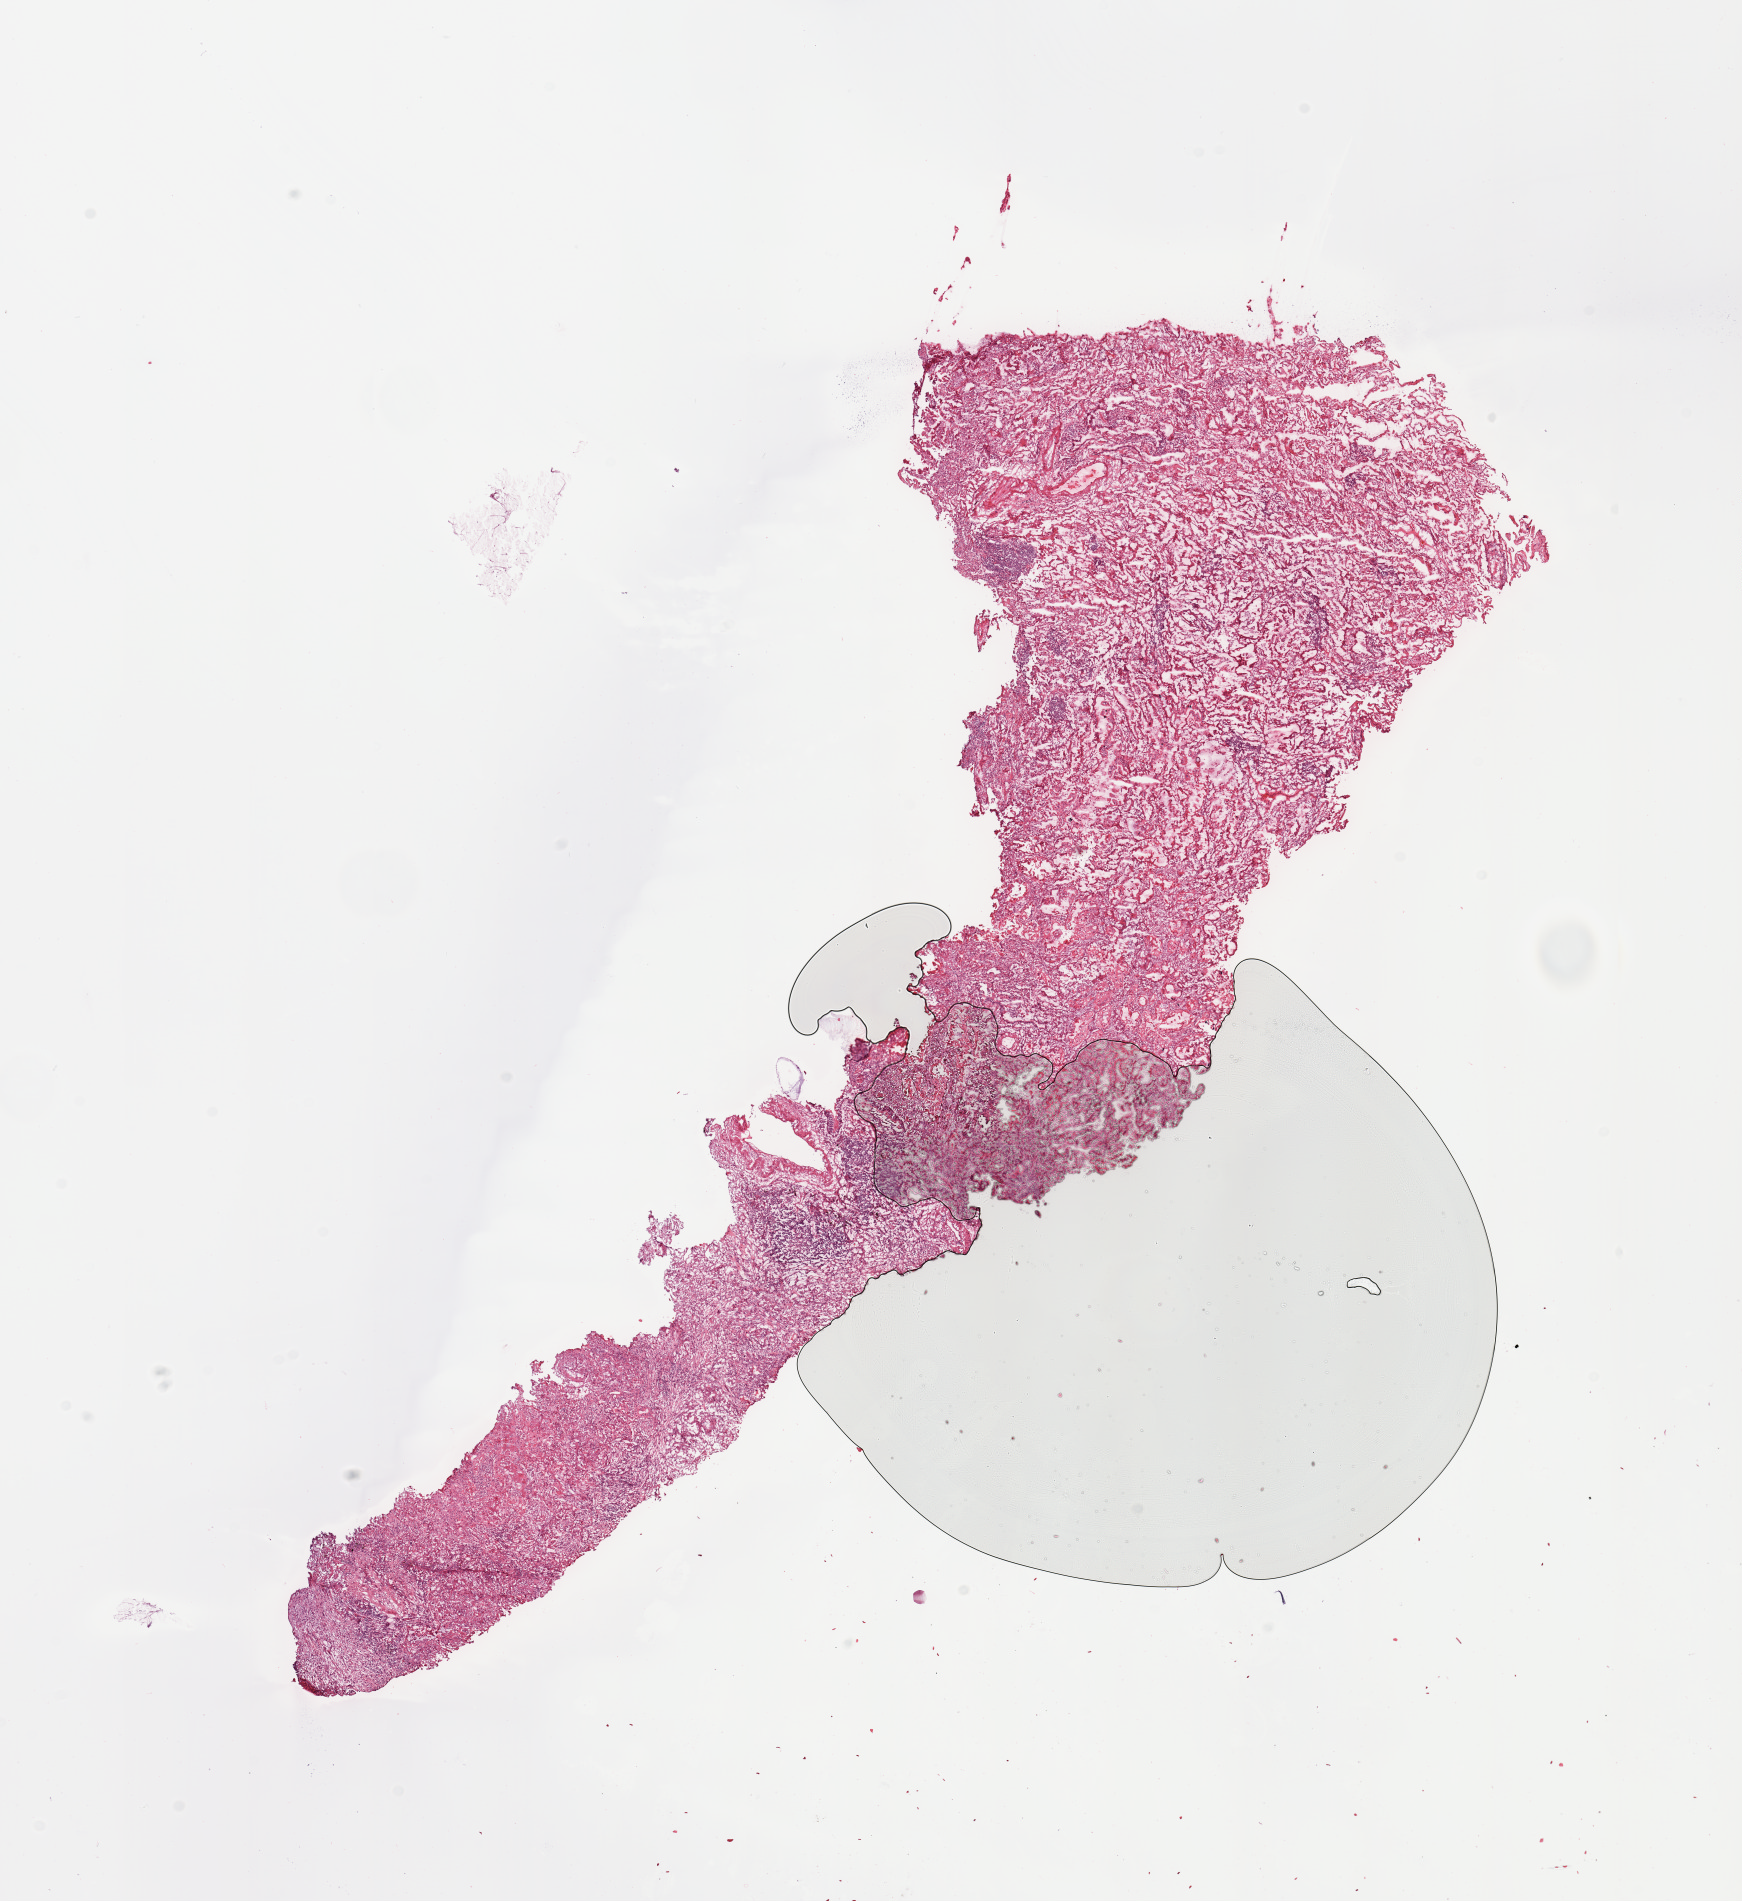
Whole-slide histology image, Hematoxylin and eosin (H&E) stained, shown as a low-resolution overview of the whole scanned area (about 13.8 x 15.0 mm); tumour tissue sample, sampled site: lung. 79-year-old male patient. Histologic grade: G2 (moderately differentiated). Slide review estimates, as recorded: tumour nuclei 80%, necrosis 0%.
Diagnosis: Adenocarcinoma, NOS. Primary tumour site (as recorded): right lower lobe. AJCC pathologic stage: IIA.